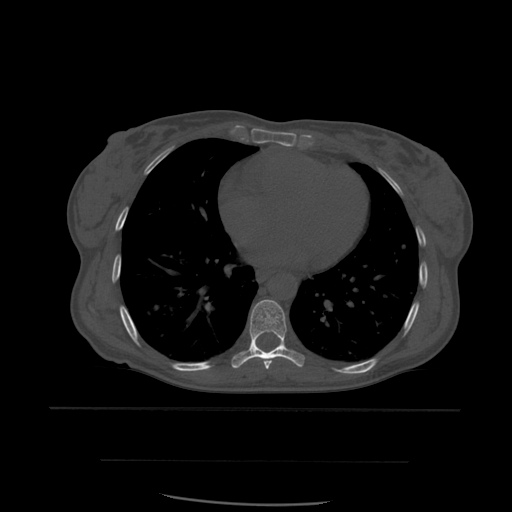
CT including the spine, one axial slice. Position 358 of 574 along the scan axis. Bone window (W 1800 / L 400 HU). 512 × 512 image matrix. Patient age 48 years. Case-level facts recorded for this patient, not image findings: primary cancer: lung; vertebrae with lytic lesions (as recorded): T11.
Structures marked on this image (semi-automatic segmentation, software-assisted and operator-edited):
- T6 vertebra: bounding box (x1, y1, x2, y2) in pixels: (251, 336, 254, 340)
- T7 vertebra: (264, 361, 272, 370)
- T8 vertebra: (232, 300, 305, 369)